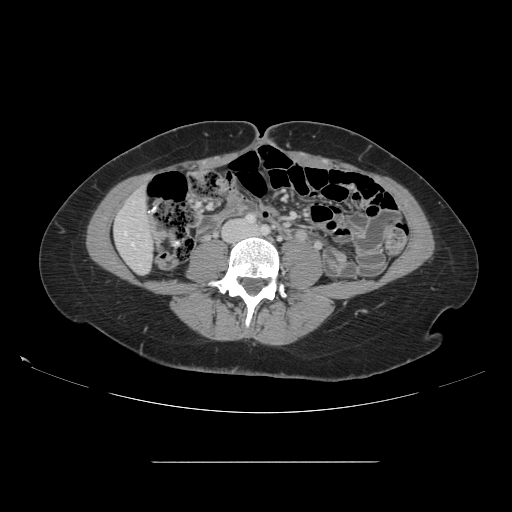
Contrast-enhanced abdominal CT, one axial slice; slice 23 of 151 in the series (ordered by position); soft-tissue window (W 400 / L 40 HU); 2.5 mm slice thickness; 512 × 512 image matrix. Female patient, age 46 years. From the clinical record (not read from this slice): diagnosis: colorectal cancer liver metastases, imaged before liver resection; multiple liver metastases: yes; largest metastasis: 3 cm; disease in both lobes: yes.
Structures marked on this image (manually delineated by an expert):
- liver: box from (x=115, y=190) to (x=153, y=273) px
- planned liver remnant (the part of the liver to remain after resection): (x=116, y=190)–(x=153, y=273)